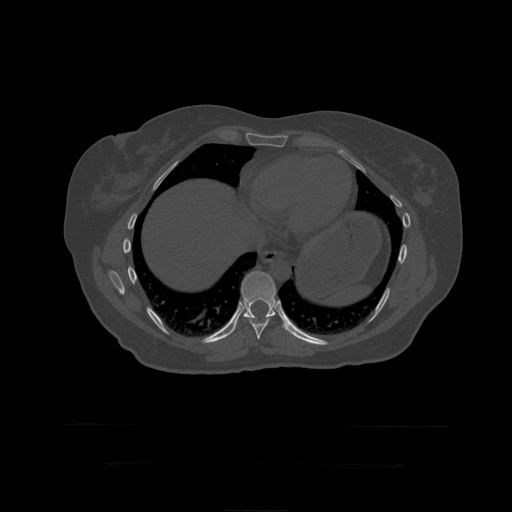
CT including the spine, one axial slice. Position 251 of 399 along the scan axis. Reconstruction kernel STANDARD. 120 kVp. Bone window (W 1800 / L 400 HU). 512 × 512 image matrix. Patient age 41 years. Case-level facts recorded for this patient, not image findings: primary cancer: breast.
Structures marked on this image (semi-automatically segmented with operator editing):
- T10 vertebra: bounding box <241,271,277,322> (left, top, right, bottom; pixels)
- T9 vertebra: <249,317,270,340>